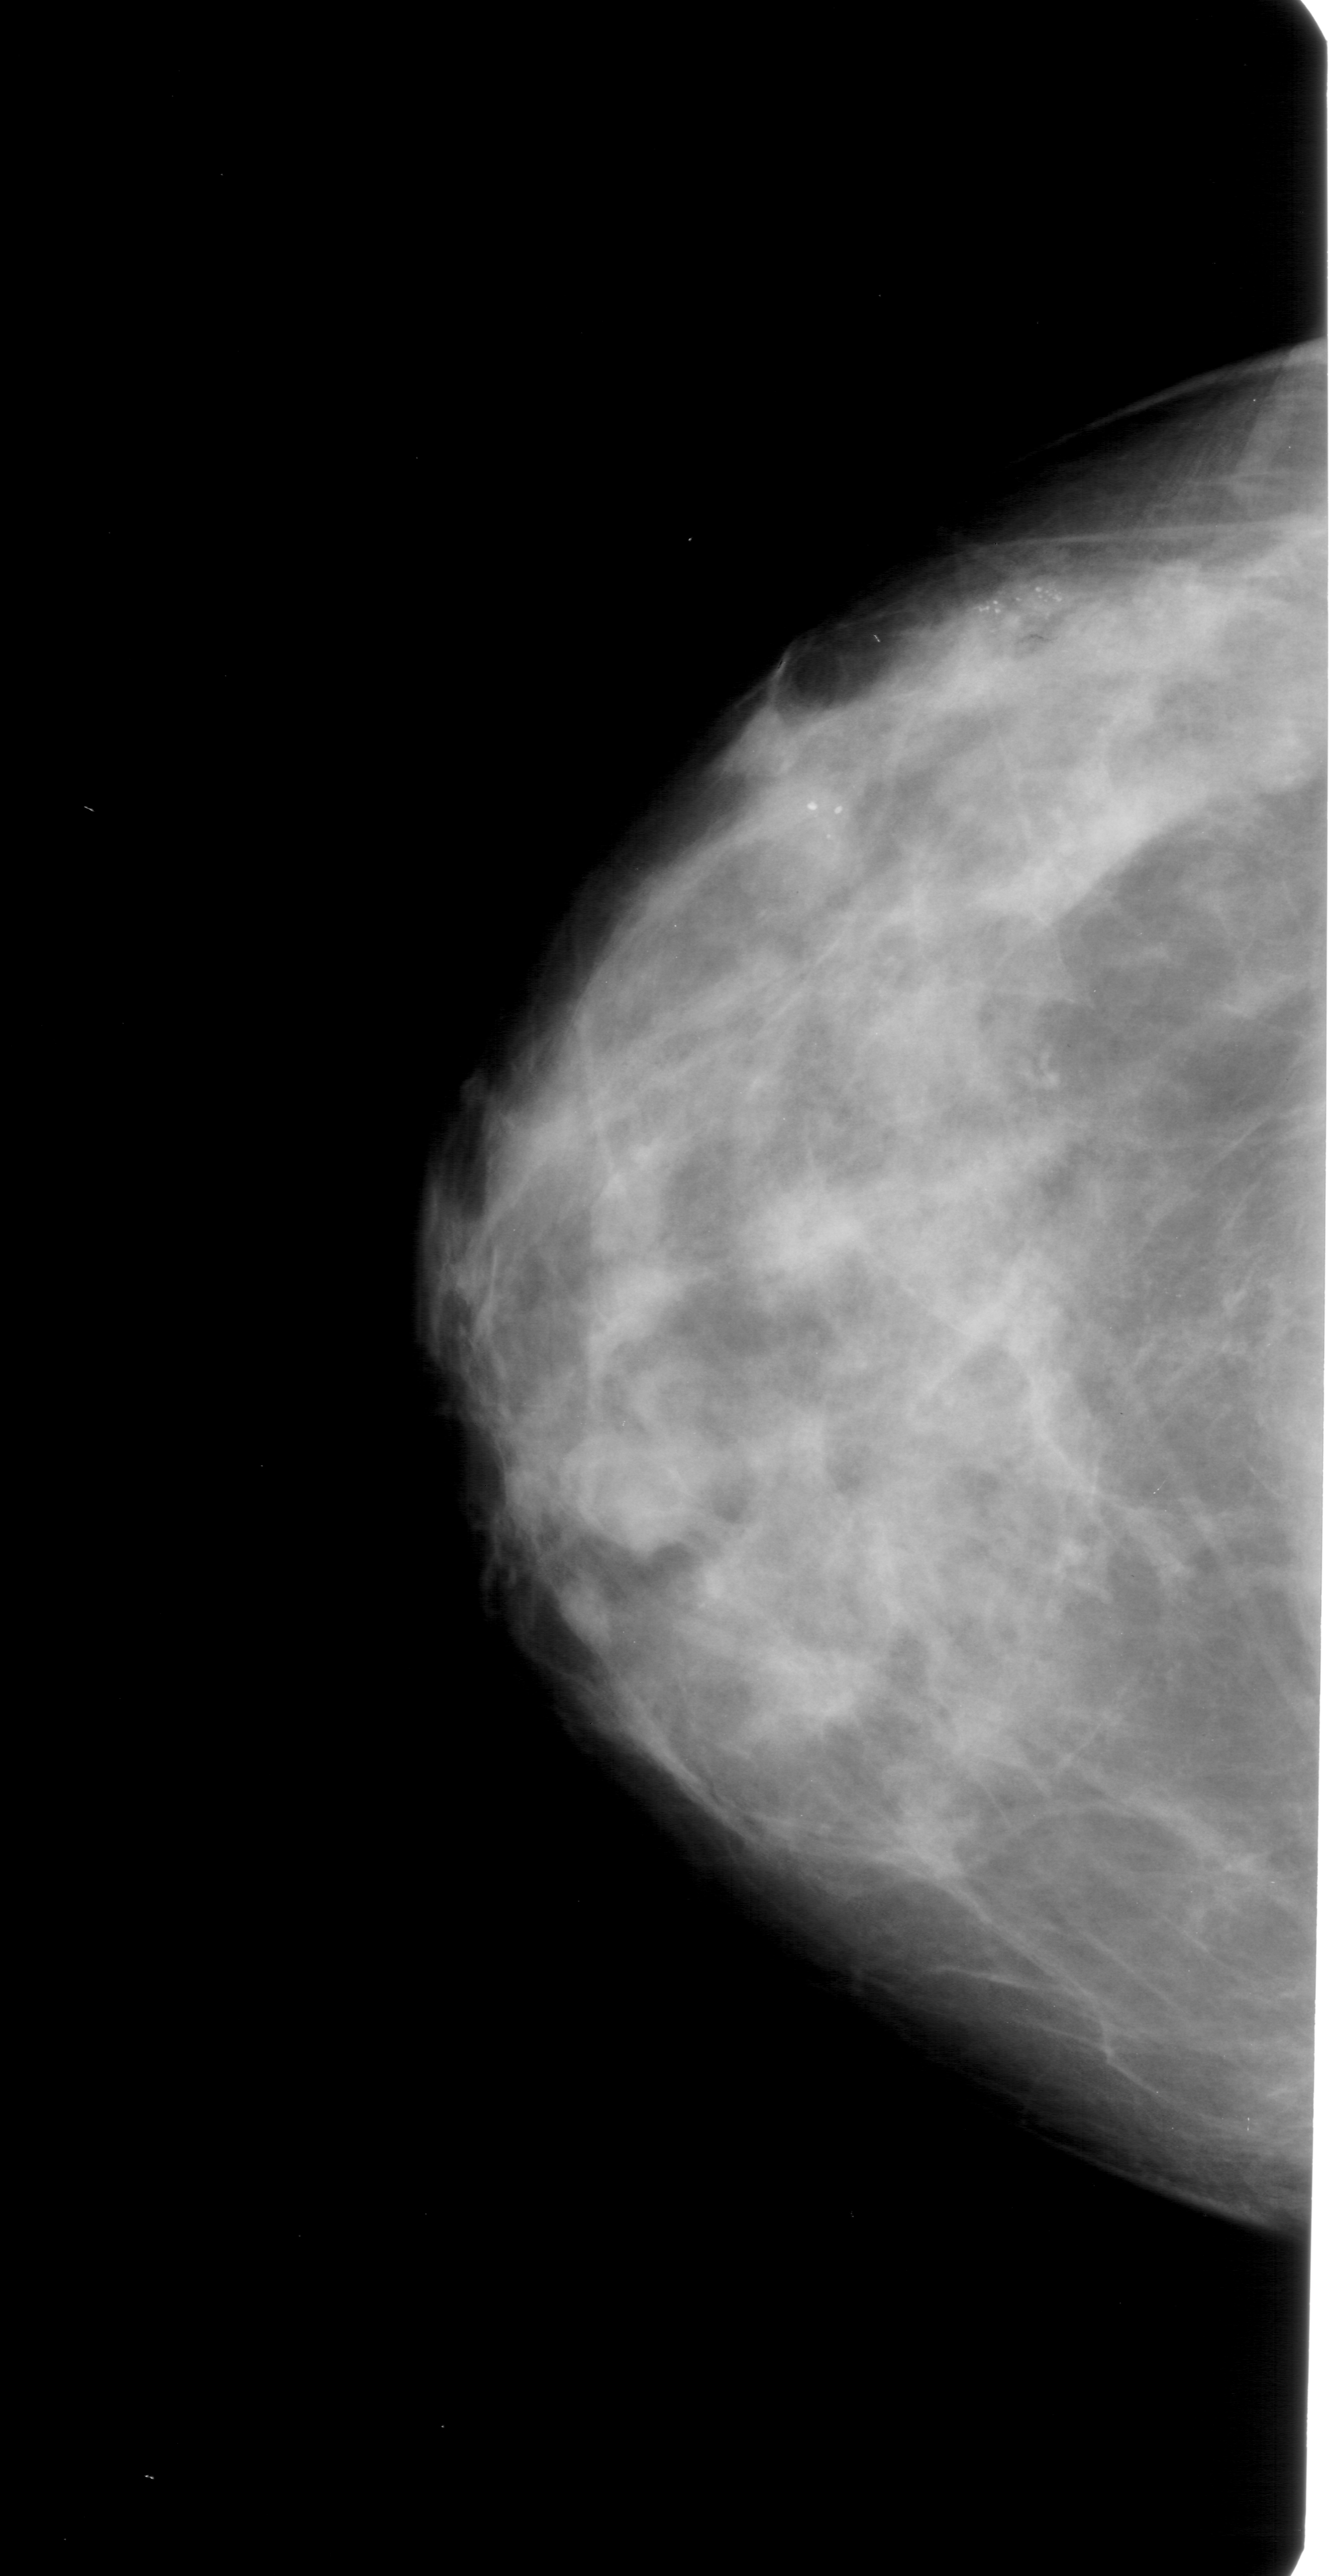
Digitized screen-film mammogram. Left breast. Craniocaudal (CC) view. Breast composition: extremely dense (BI-RADS density category 4 of 4). 1329 × 2576 image matrix.
Expert-marked regions of interest on this image (one box per marked abnormality):
- calcifications, morphology pleomorphic, distribution clustered; BI-RADS assessment category 4; subtlety rating 4 on a 1 (subtle) to 5 (obvious) scale; pathology result (as recorded, not read from the image): malignant: bounding box [x1, y1, x2, y2] px = [957, 566, 1074, 651]